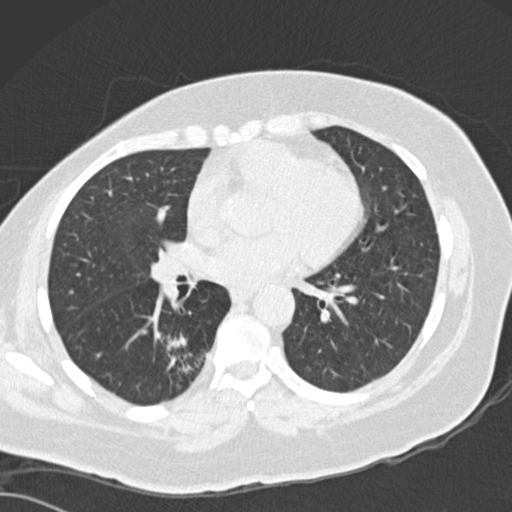
Axial slice from a low-dose chest CT screening exam. First (baseline) screen. Lung window (W 1500 / L -600 HU). 2 mm slice thickness. 120 kVp. Slice 88 of 162 in the series. Female, age 66 years at enrolment. Current smoker at enrolment.
- Expert-annotated lung lesion, bounding box [x1, y1, x2, y2] px = [153, 324, 222, 395].
- The screening reader recorded 3 non-calcified nodules or masses ≥4 mm on this exam (left lower lobe, left lower lobe, right lower lobe); which of them this box marks is not recorded.
- Official screen result: positive, change unspecified: nodule(s) >= 4 mm or enlarging nodule(s), mass(es), or other non-specific abnormalities suspicious for lung cancer.
- Lung cancer was diagnosed 67 days after this screen: adenocarcinoma, NOS, right lower lobe, well differentiated (G1), stage IB (AJCC 6th edition), 55 mm at pathology.